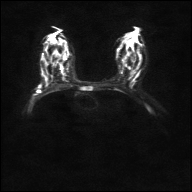
Breast MRI, one axial slice. Position 19 of 36 along the scan axis. Diffusion-weighted series; image 2 of 4 stored at this slice position (different b-values; order by instance number). 1.5 T. 4 mm slice thickness. 192 × 192 image matrix, field of view 360 × 360 mm. Female patient.
Outlined on this slice (expert manual segmentation):
- tumour on diffusion-weighted imaging: box from (x=37, y=84) to (x=44, y=87) px